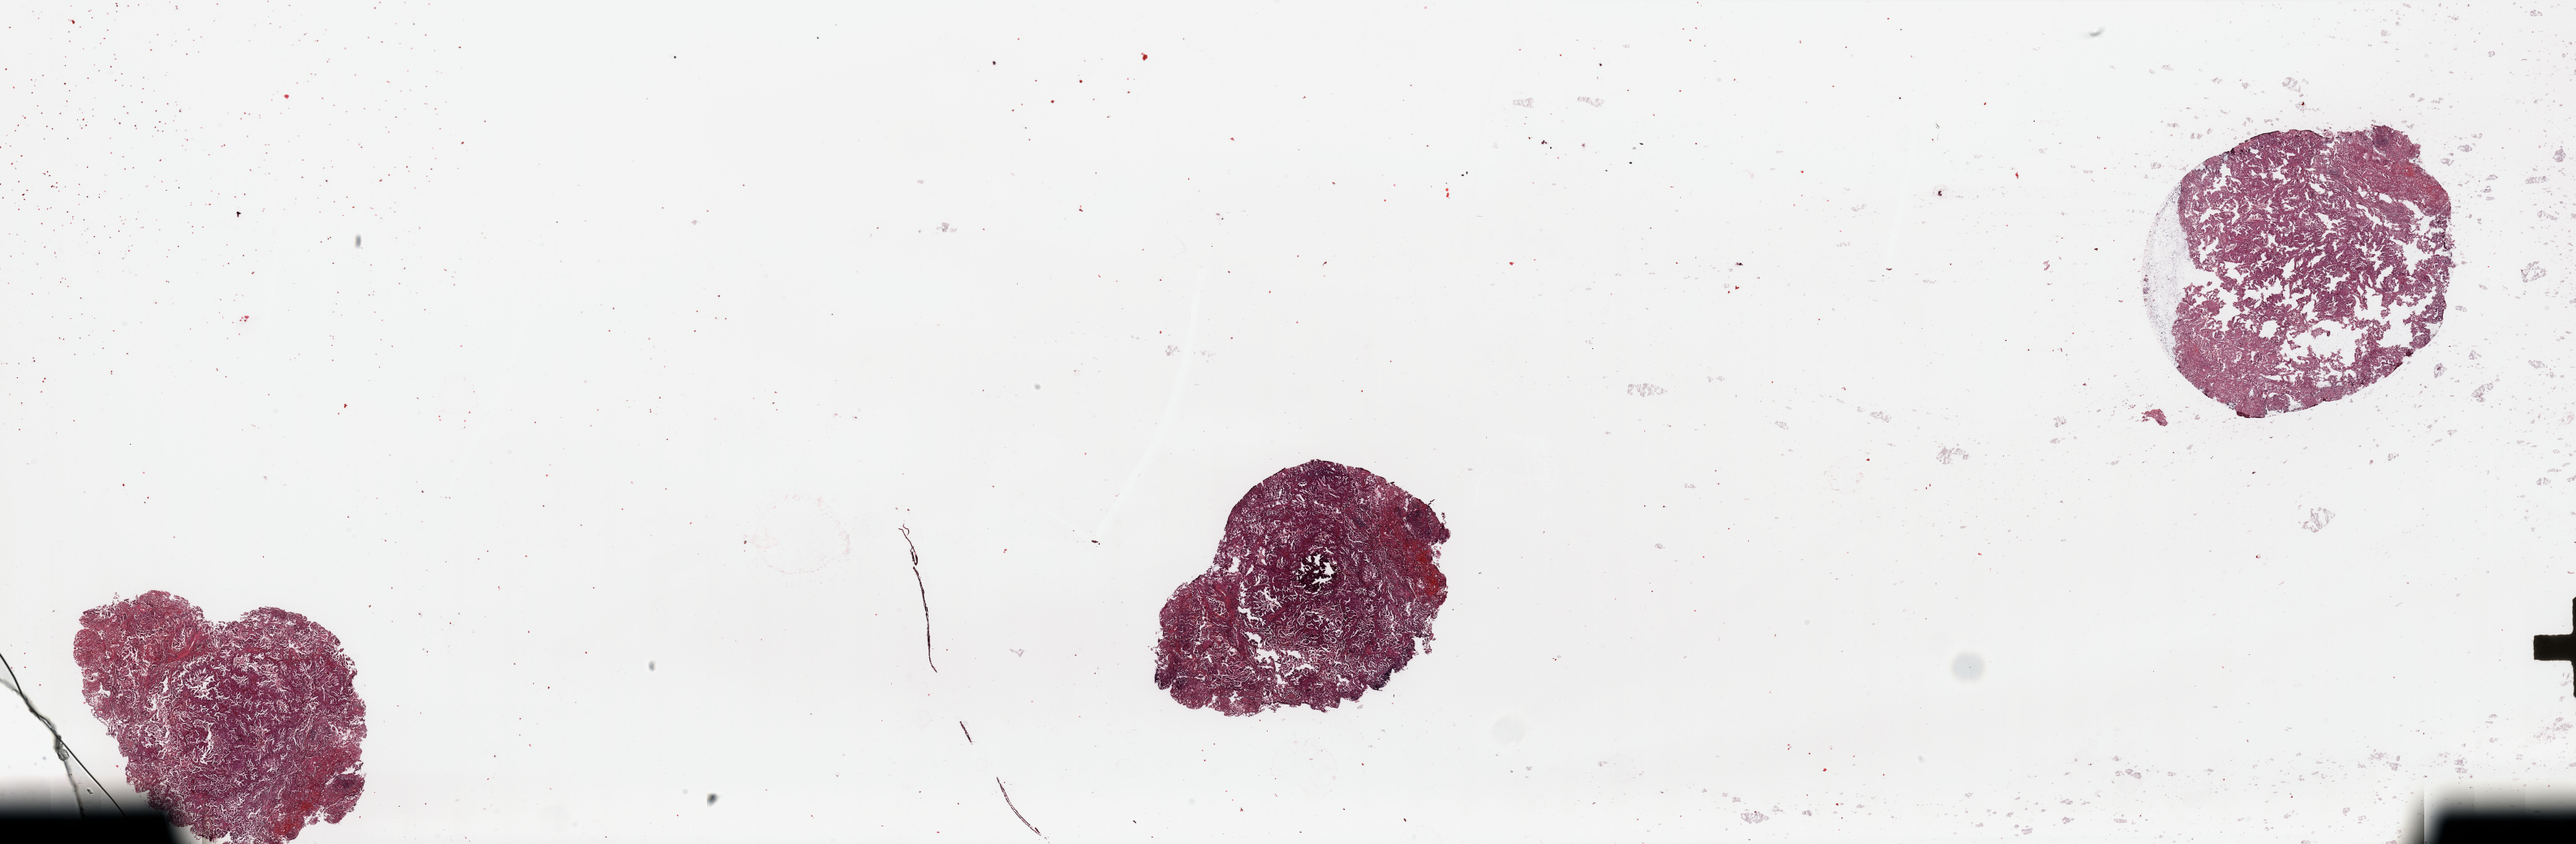
Whole-slide histology image, Hematoxylin and eosin (H&E) stained — a low-resolution overview of the entire scanned area, about 50.2 x 16.5 mm (from a 20x scan), tumour tissue sample, sampled site: lung. 59-year-old male patient. Histologic grade: G2 (moderately differentiated). Composition of this section per pathologist review: tumour nuclei 70%, necrosis 5%.
Histologic diagnosis: Adenocarcinoma, NOS. AJCC pathologic stage: IIIA.